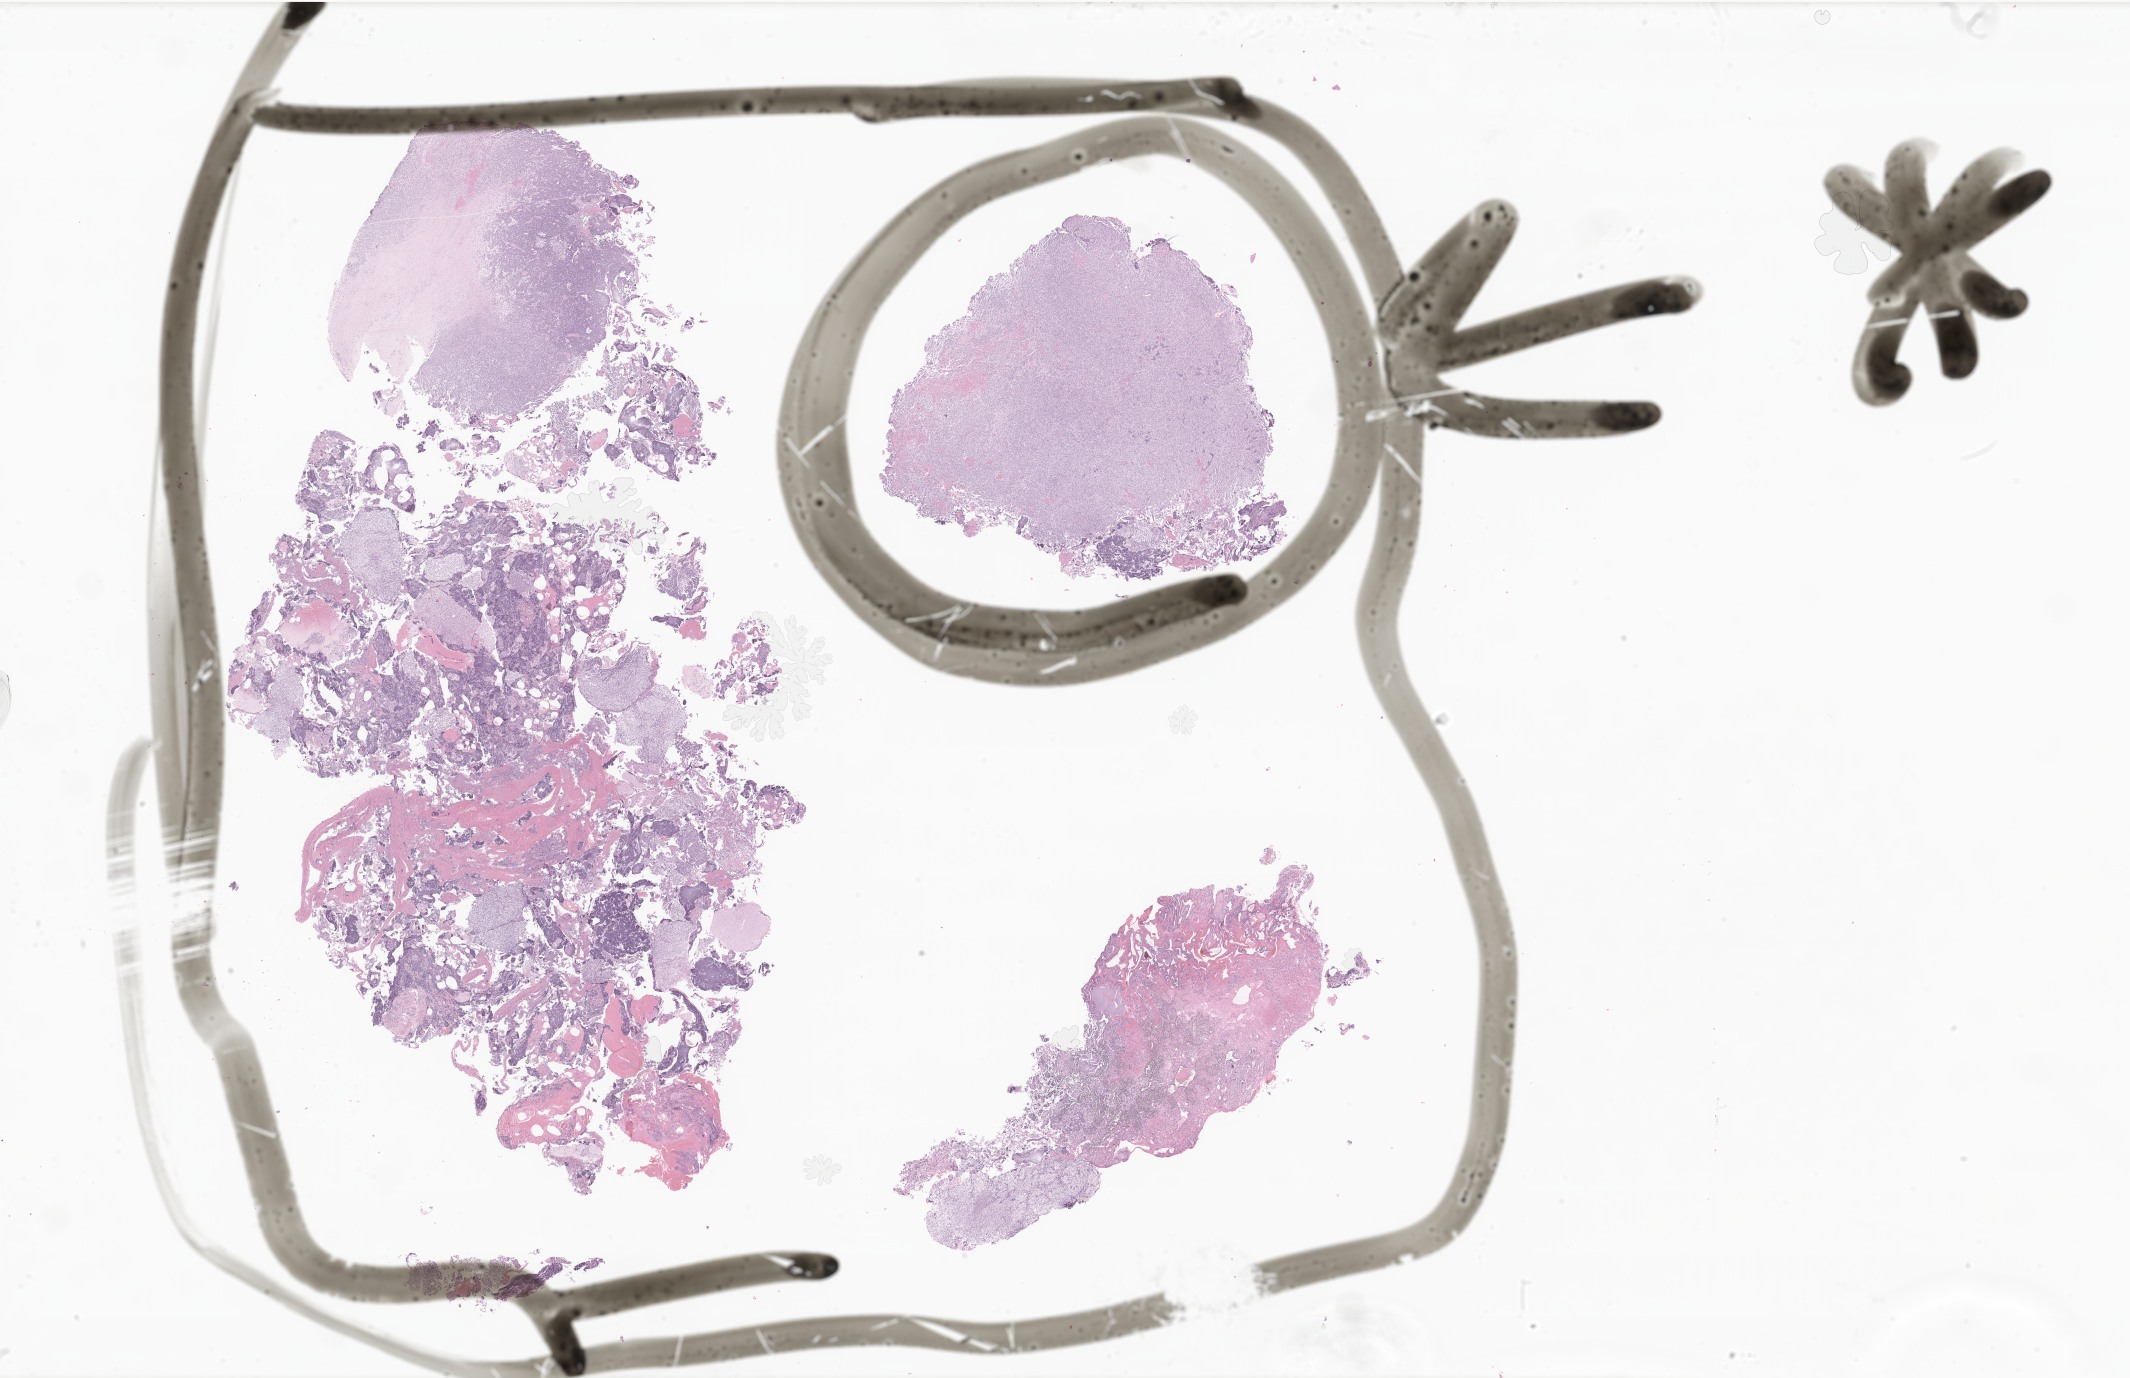
Whole-slide image, hematoxylin and eosin (H&E) stain of tumor tissue from the brain — shown as a low-resolution overview of the whole scanned area (about 35.9 x 23.2 mm). Formalin-fixed paraffin-embedded section. Patient: male, age 76 months (6 years 4 months).
Recorded diagnosis: Medulloblastoma, NOS.